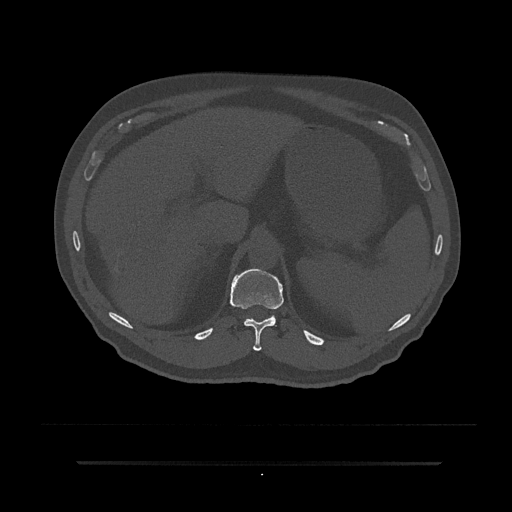
CT including the spine, one axial slice. Slice 256 of 797 in the series (ordered by position). 120 kVp. Bone window (W 1800 / L 400 HU). 0.5 mm slice thickness. 512 × 512 image matrix, field of view 464 × 464 mm. Patient: male, 59 years. Case-level facts recorded for this patient, not image findings: primary cancer: bile ducts; vertebrae with lytic lesions (as recorded): T10.
Structures marked on this image (semi-automatically segmented with operator editing):
- T11 vertebra: bounding box <230,268,284,351> (left, top, right, bottom; pixels)
- T12 vertebra: <245,315,276,321>